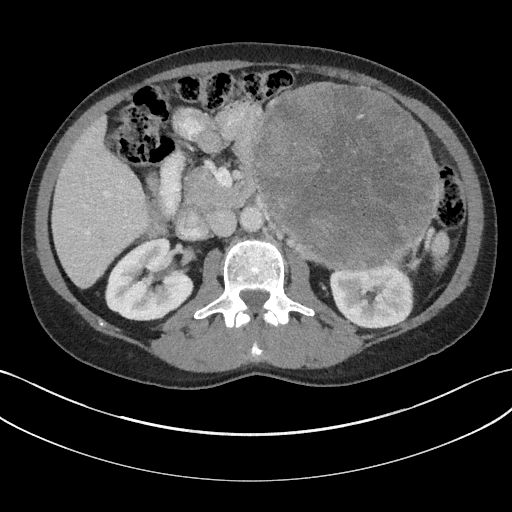
Contrast-enhanced abdominal CT, one axial slice; slice 97 of 147 in the series (ordered by position); 100 kVp; soft-tissue window (W 400 / L 40 HU); 3 mm slice thickness; 512 × 512 image matrix, field of view 384 × 384 mm. Male patient, age 58 years. Case-level facts recorded for this patient, not image findings: diagnosis: adrenocortical carcinoma; tumour side: left adrenal; tumour size at pathology: 22 cm; Ki-67 index: 26 %; stage (as recorded): 2.
Annotated regions visible in this slice (semi-automatically segmented with operator editing):
- mass: box from (x=254, y=85) to (x=438, y=265) px